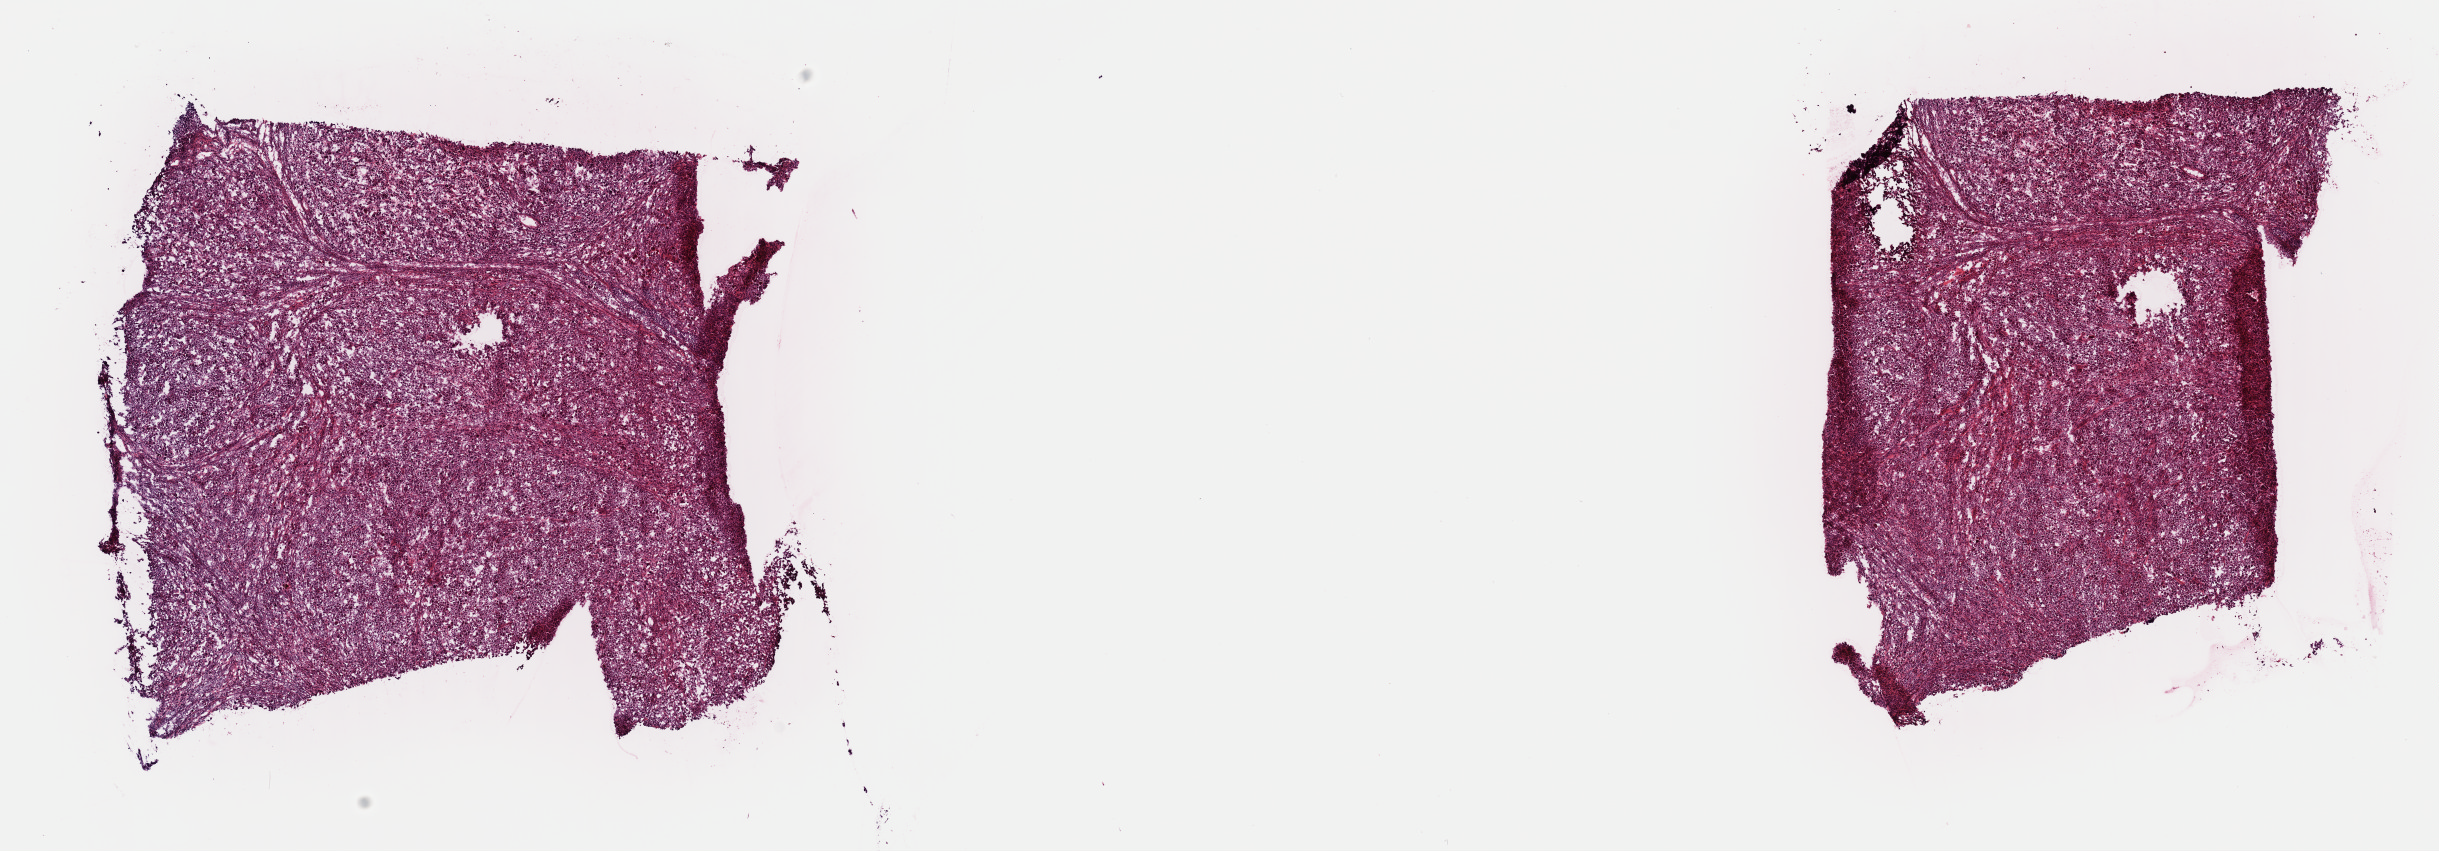
H&E-stained whole-slide image — low-resolution overview of the scanned area, about 19.3 x 6.7 mm (acquisition: 40x scan). Frozen section from the top of the tissue portion. Sample: primary tumour, bladder. Male patient; age at initial diagnosis 44 years. Histologic grade: high grade. Pathologist review of this section (percent, as recorded): tumour cells 60%, tumour nuclei 92%, normal cells 0%, stromal cells 20%, necrosis 20%. Infiltration values recorded for this section: lymphocyte infiltration 5%, monocyte infiltration 0%, neutrophil infiltration 0%.
Histologic diagnosis: Papillary transitional cell carcinoma. AJCC pathologic stage: IV (7th edition). Lymph nodes positive (case pathology): 4 of 4 examined.